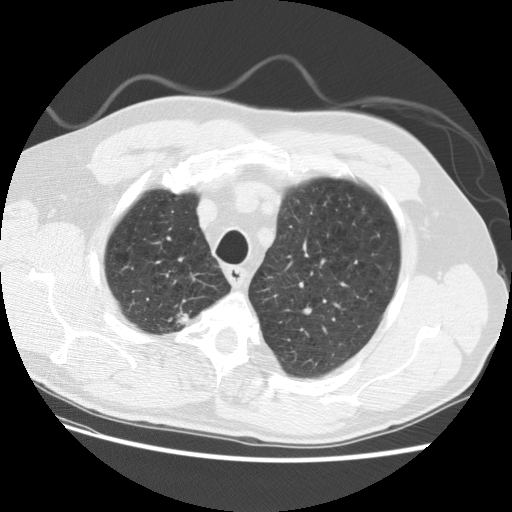
Low-dose screening chest CT, one axial slice. Slice 103 of 124 in the series (ordered by position). Reconstruction kernel STANDARD. Lung window (W 1500 / L -600 HU). 2.5 mm slice thickness. 512 × 512 image matrix.
Structures marked on this image (expert manual segmentation):
- lesion 1 (tumor, upper lobe of right lung): bounding box (x1, y1, x2, y2) in pixels: (176, 307, 191, 325)